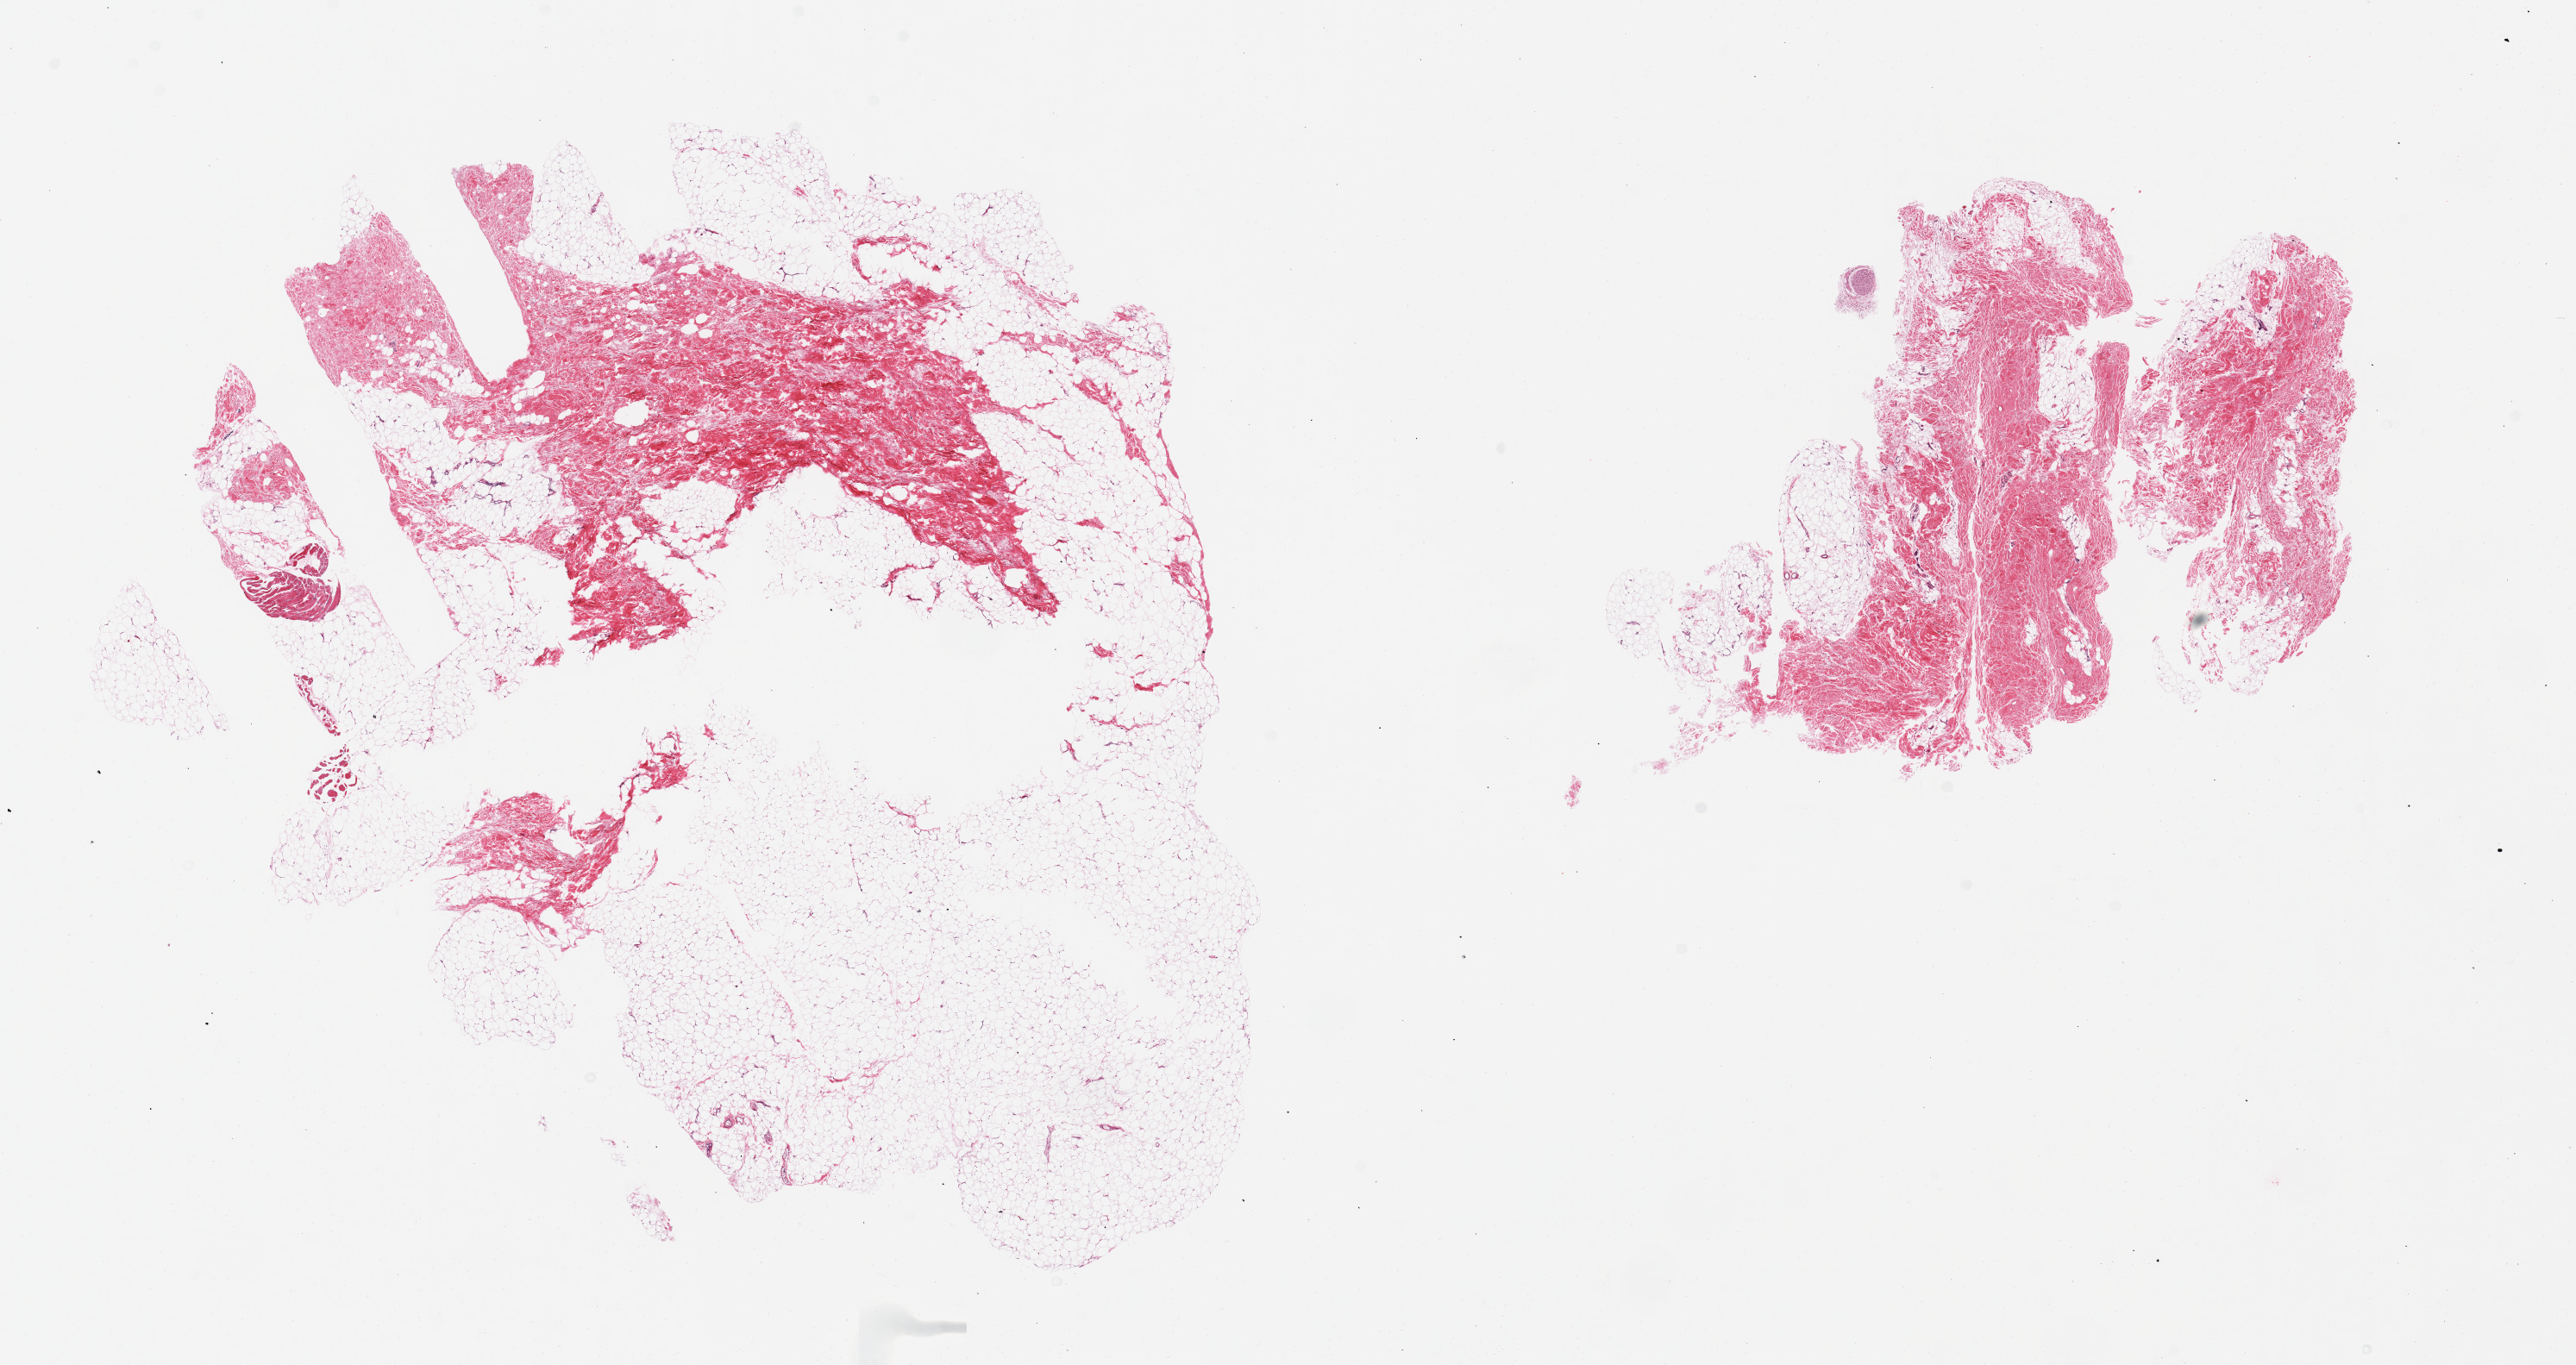
Whole-slide image, haematoxylin and eosin stain, brightfield — low-resolution overview of the scanned area, about 23.6 x 12.5 mm (slide scanned at 20x). PAXgene-fixed, paraffin-embedded tissue. Sampled site (target tissue): breast. Donor tissue sample. Donor: male.
Reviewer comment on this tissue sample: 2 pieces; fibrofatty tissue.